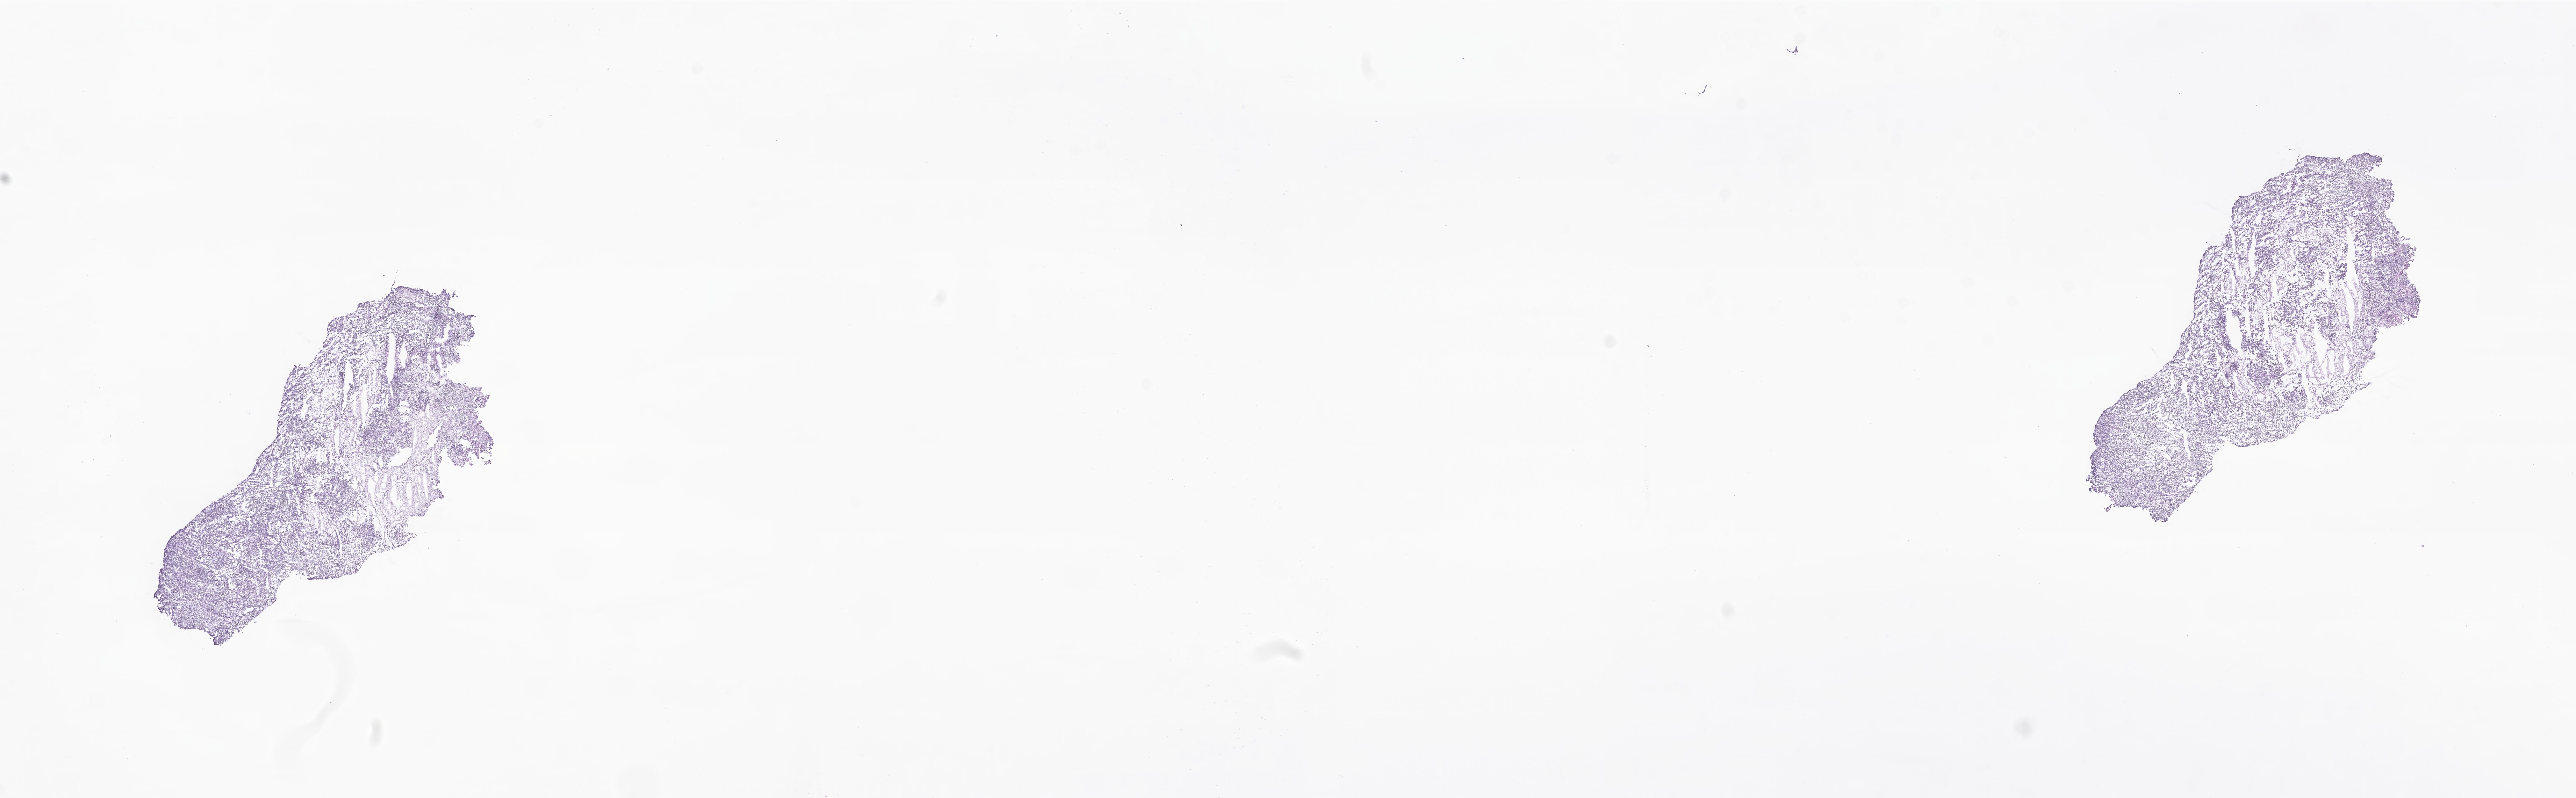
Digitized haematoxylin and eosin-stained section of tumor tissue from the brain — whole scanned area (about 31.1 x 9.6 mm) shown as a low-resolution overview; frozen section. Male patient, age 71 months (5 years 11 months).
* diagnosis: Medulloblastoma, NOS